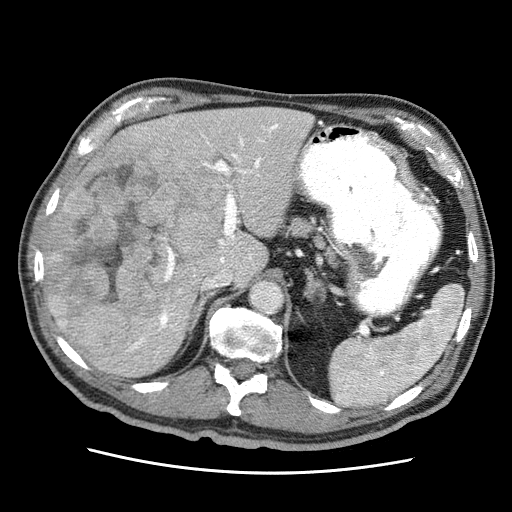
Contrast-enhanced abdominal CT (liver protocol), one axial slice; position 34 of 75 along the scan axis; reconstruction kernel STANDARD; 120 kVp; soft-tissue window (W 400 / L 40 HU); 2.5 mm slice thickness; 512 × 512 image matrix, field of view 360 × 360 mm. From the clinical record (not read from this slice): diagnosis: hepatocellular carcinoma (patient treated with transarterial chemoembolisation; whether this scan precedes or follows treatment is not stated here); TNM stage (as recorded): Stage-IIIA; Child-Pugh class: A; tumour differentiation: well differentiated; tumour nodularity: multinodular.
Annotated regions visible in this slice (semi-automatic segmentation, software-assisted and operator-edited):
- liver parenchyma outside the tumour (the mass and vessels are separate outlines, so this box may not span the whole liver): box from (x=44, y=106) to (x=313, y=376) px
- mass: (x=46, y=135)–(x=232, y=353)
- liver vessels: (x=169, y=124)–(x=278, y=331)